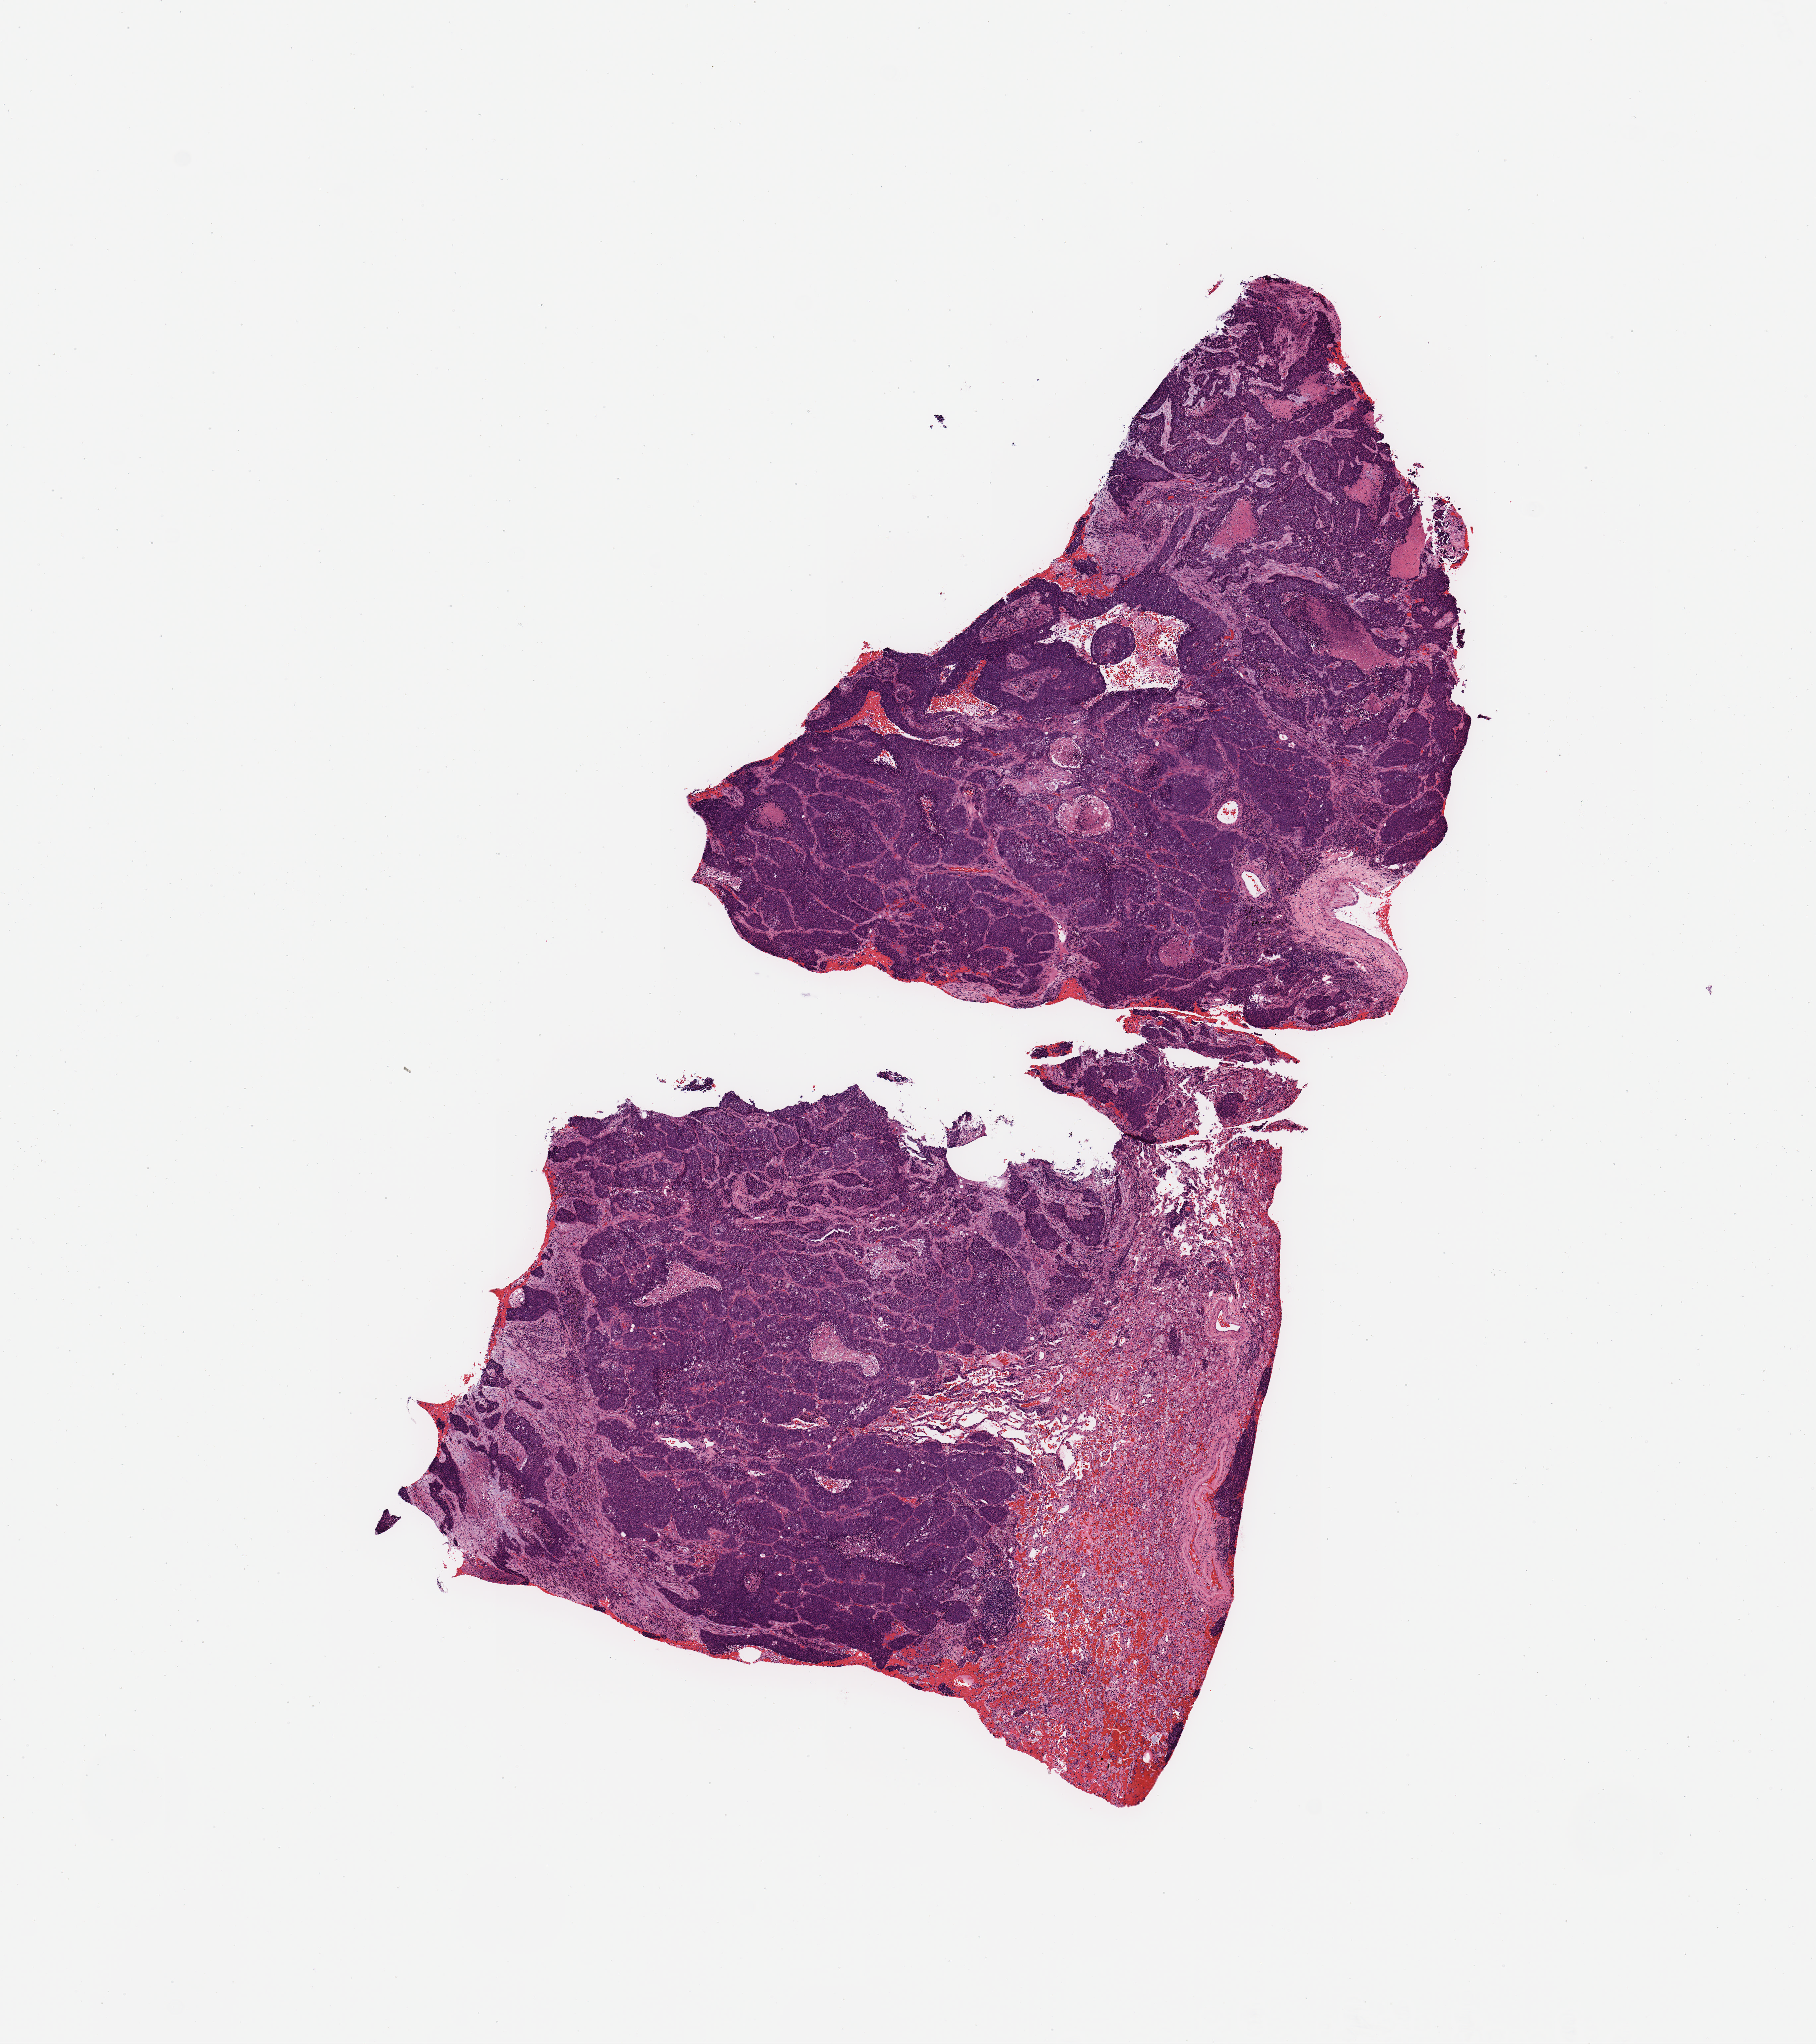
H&E whole-slide image — shown as a low-resolution overview of the whole scanned area (about 10.8 x 12.2 mm, from a 20x scan), tumour tissue sample, lung. Patient: male, age 54 years. Histologic grade: G2 (moderately differentiated).
- AJCC pathologic stage: IIA
- primary tumour site (as recorded): left upper lobe
- histologic diagnosis: Squamous cell carcinoma, NOS